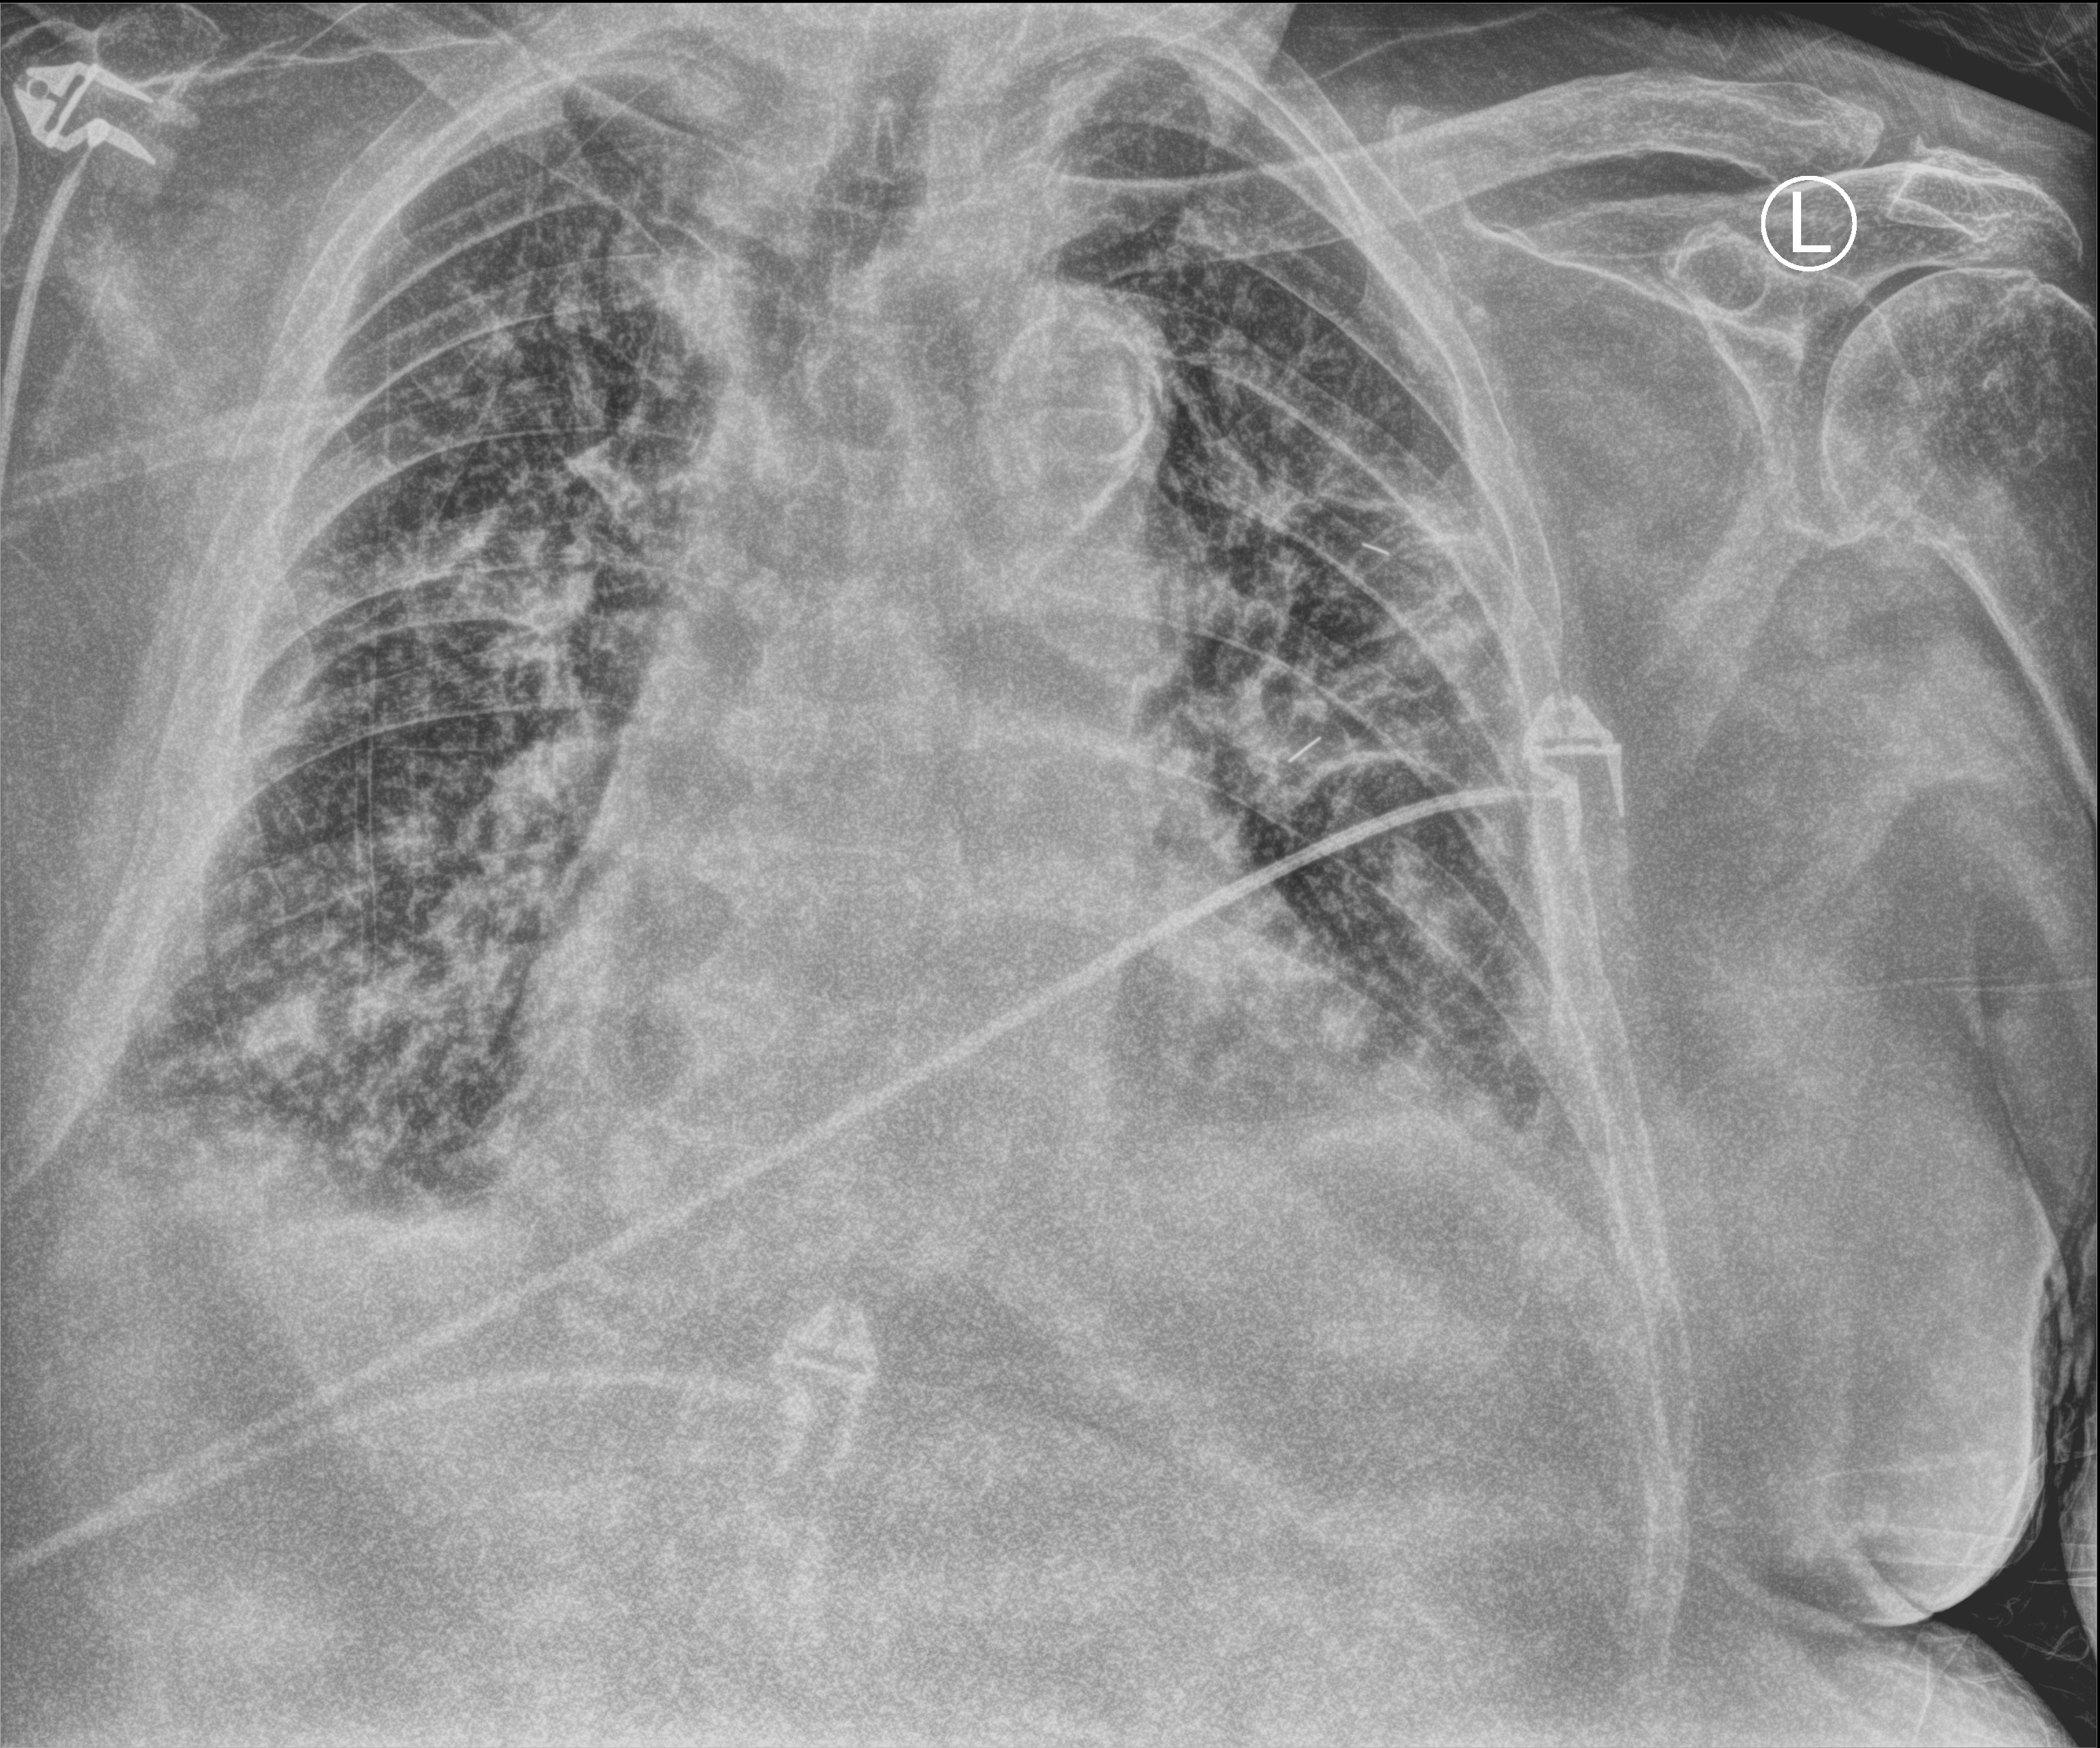
Chest X-ray (portable); anteroposterior (AP) projection. Male patient hospitalised with COVID-19, age 75–90 years.
Hospital-stay facts (about this admission, not read from this image; timing relative to this image not recorded):
- mechanically ventilated during this hospital stay: no